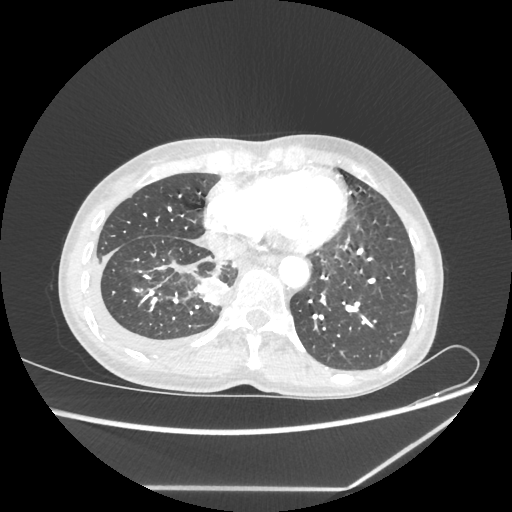
Chest CT, one axial slice. Position 66 of 237 along the scan axis. Reconstruction kernel STANDARD. 80 kVp. Lung window (W 1500 / L -600 HU). 1.25 mm slice thickness. 512 × 512 image matrix, field of view 364 × 364 mm. Female patient, age 59 years. Case-level facts recorded for this patient, not image findings: clinical TNM (as recorded): T1c N1 M1.
Outlined on this slice (rectangle marked by the reading radiologist):
- lung tumour (recorded histology: adenocarcinoma): bounding box (x1, y1, x2, y2) in pixels: (195, 273, 228, 306)